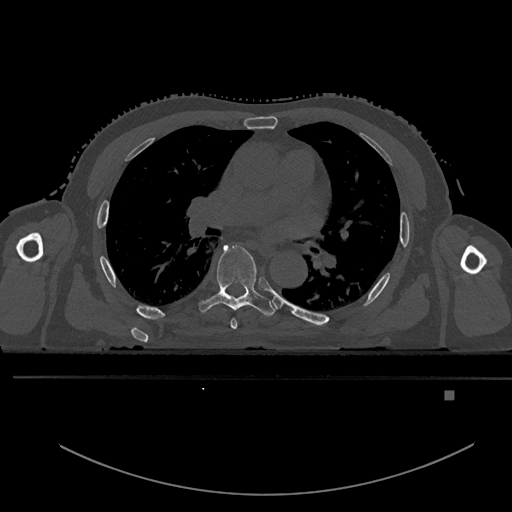
CT including the spine, one axial slice; slice 314 of 969 in the series (ordered by position); bone window (W 1800 / L 400 HU); 0.5 mm slice thickness; 512 × 512 image matrix, field of view 456 × 456 mm. Male patient, age 82 years. From the clinical record (not read from this slice): primary cancer: prostate; vertebrae with lytic lesions (as recorded): T11, T9, T8, T2.
Structures marked on this image (semi-automatic segmentation, software-assisted and operator-edited):
- T5 vertebra: box from (x=230, y=318) to (x=238, y=330) px
- T6 vertebra: (x=199, y=244)–(x=277, y=317)